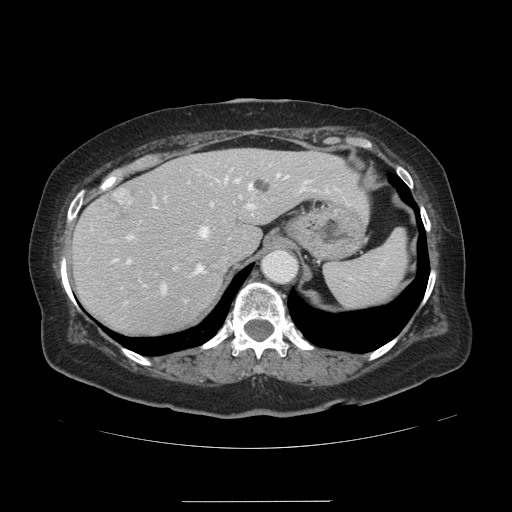
Contrast-enhanced abdominal CT, one axial slice; slice 98 of 141 in the series (ordered by position); 120 kVp; intravenous contrast given; soft-tissue window (W 400 / L 40 HU); 2.5 mm slice thickness; 512 × 512 image matrix, field of view 393 × 393 mm. Female patient, age 74 years. Case-level facts recorded for this patient, not image findings: diagnosis: colorectal cancer liver metastases, imaged before liver resection; multiple liver metastases: yes; largest metastasis: 7 cm; disease in both lobes: yes.
Structures marked on this image (outlined manually by an expert reader):
- hepatic veins: bounding box (x1, y1, x2, y2) in pixels: (152, 174, 279, 275)
- liver: (74, 149, 367, 337)
- planned liver remnant (the part of the liver to remain after resection): (74, 149, 367, 337)
- portal vein (with intrahepatic branches): (127, 176, 315, 294)
- liver metastasis: (253, 178, 271, 193)
- liver metastasis: (99, 186, 134, 215)